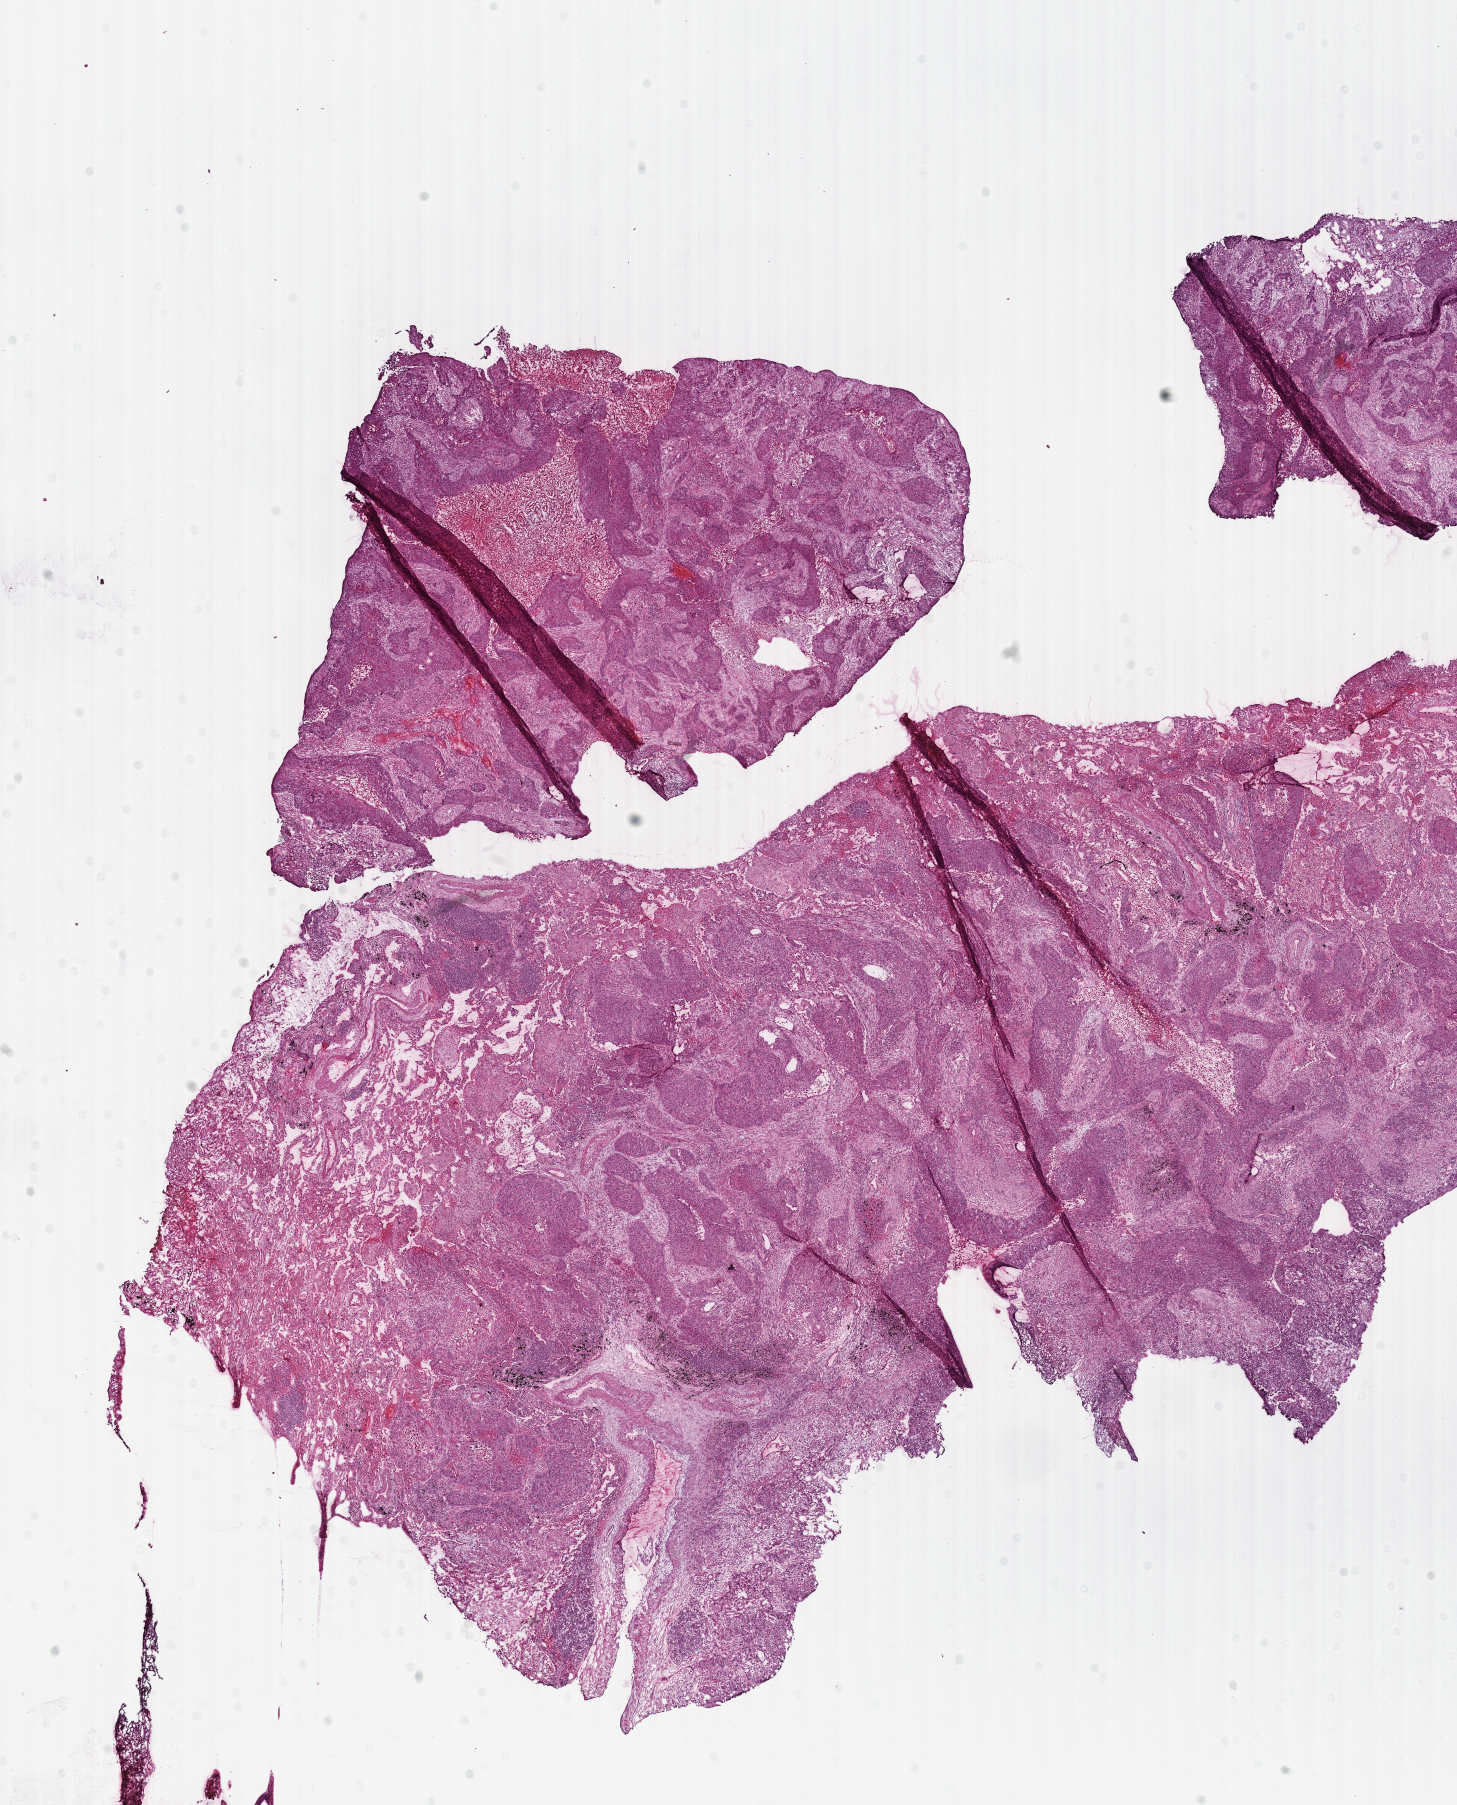
Digitized H&E-stained tissue section (whole slide), a low-resolution overview of the entire scanned area, about 11.5 x 14.2 mm (from a 40x scan). Frozen section from the top of the tissue portion. Primary tumour sample from the lung. Patient: female, age at initial diagnosis 62 years. Composition of this section per pathologist review: tumour cells 75%, tumour nuclei 60%, normal cells 10%, stromal cells 15%, necrosis 0%.
Laterality: right. AJCC pathologic stage: IA (7th edition). TNM: T1a N0 M0. Histologic diagnosis: Squamous cell carcinoma, NOS.